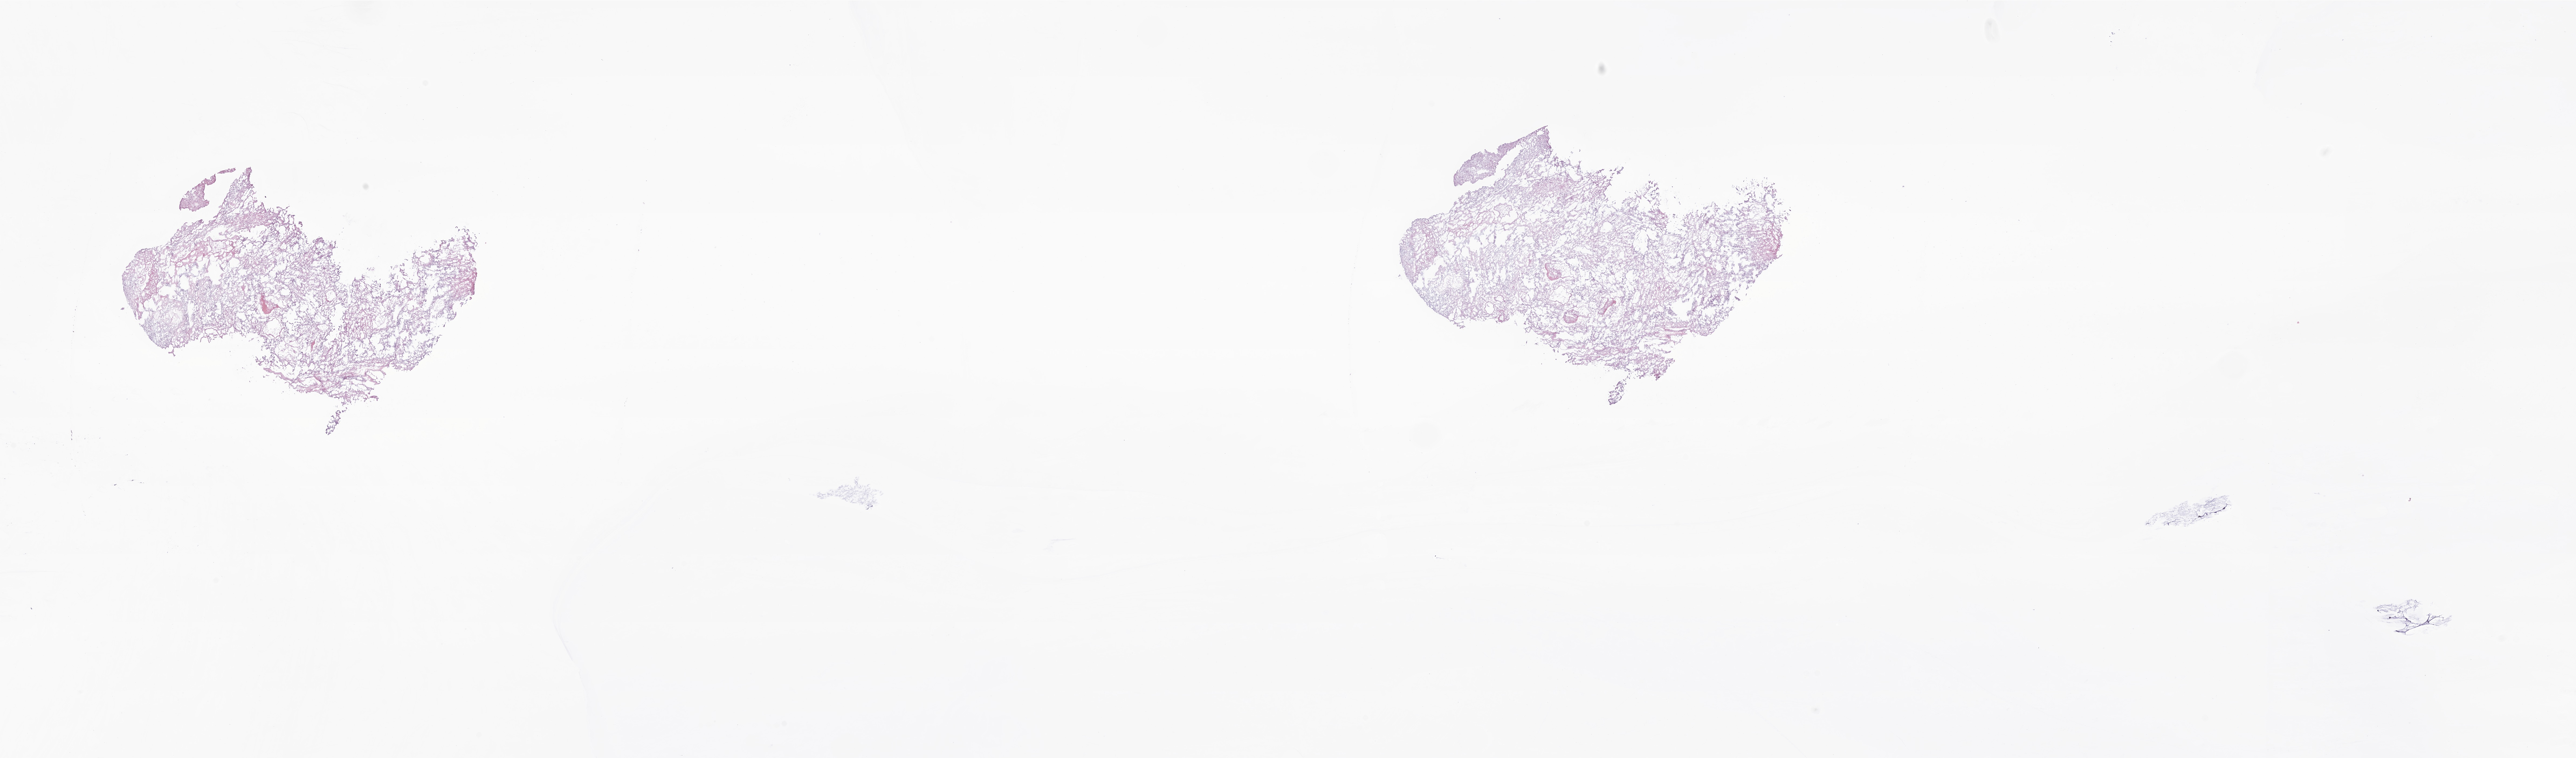
Whole-slide image, haematoxylin and eosin stain of tumor tissue from the brain, a low-resolution overview of the entire scanned area, about 40.2 x 11.8 mm; cryosection (OCT / tissue freezing medium). Female patient, age 151 months (12 years 7 months).
• diagnosis (ICD-O-3 morphology term): Pilocytic astrocytoma